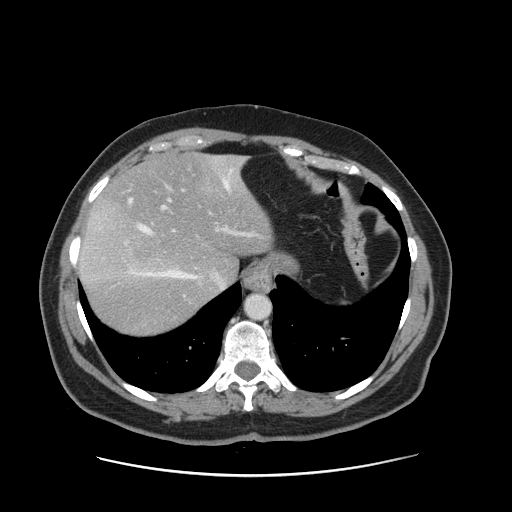
Contrast-enhanced abdominal CT, one axial slice; slice 121 of 161 in the series (ordered by position); 120 kVp; intravenous contrast given; soft-tissue window (W 400 / L 40 HU); 2.5 mm slice thickness; 512 × 512 image matrix. Female patient, age 62 years. Case-level facts recorded for this patient, not image findings: diagnosis: colorectal cancer liver metastases, imaged before liver resection; multiple liver metastases: no; largest metastasis: 2.5 cm; disease in both lobes: no.
Structures marked on this image (outlined manually by an expert reader):
- hepatic veins: bounding box <128,158,244,289> (left, top, right, bottom; pixels)
- liver: <79,155,273,337>
- planned liver remnant (the part of the liver to remain after resection): <96,154,272,280>
- portal vein (with intrahepatic branches): <160,188,258,237>